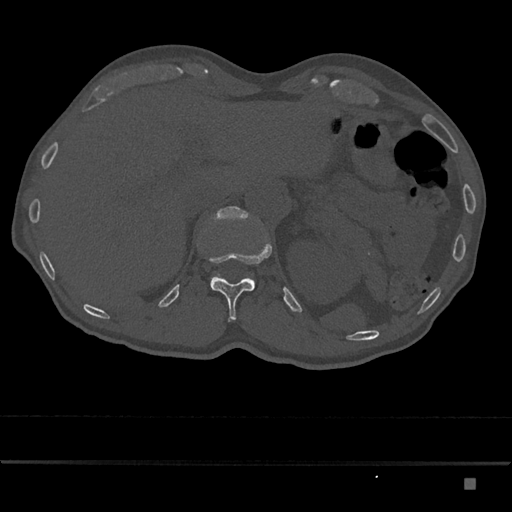
CT including the spine, one axial slice; slice 597 of 797 in the series (ordered by position); 120 kVp; bone window (W 1800 / L 400 HU); 0.5 mm slice thickness; 512 × 512 image matrix. Male patient, age 72 years. Case-level facts recorded for this patient, not image findings: primary cancer: prostate.
Outlined on this slice (semi-automatic segmentation, software-assisted and operator-edited):
- L1 vertebra: bounding box <210,207,255,288> (left, top, right, bottom; pixels)
- T12 vertebra: <209,243,272,322>